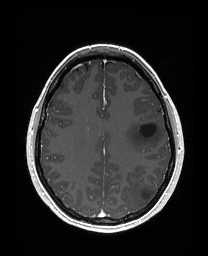
Brain MRI from a brain-tumour surgery series, one axial slice. Position 106 of 176 along the scan axis. T1-weighted post-contrast. 1 mm slice thickness. 208 × 256 image matrix, field of view 203 × 250 mm. Case-level facts recorded for this patient, not image findings: histopathology: Astrocytoma; WHO grade: 3; IDH mutation: yes.
Annotated regions visible in this slice (manually delineated by an expert):
- tumour: bounding box [x1, y1, x2, y2] px = [124, 120, 162, 151]